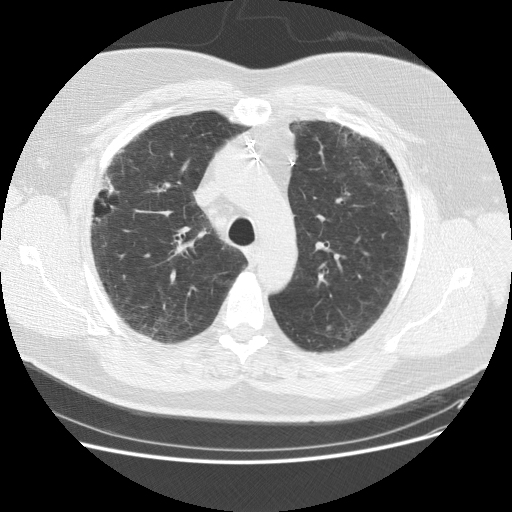
Low-dose screening chest CT, one axial slice; slice 115 of 151 in the series (ordered by position); 120 kVp; lung window (W 1500 / L -600 HU); 2.5 mm slice thickness; 512 × 512 image matrix.
Outlined on this slice (expert manual segmentation):
- lesion 2 (tumor, upper lobe of right lung): bounding box (x1, y1, x2, y2) in pixels: (98, 176, 115, 198)